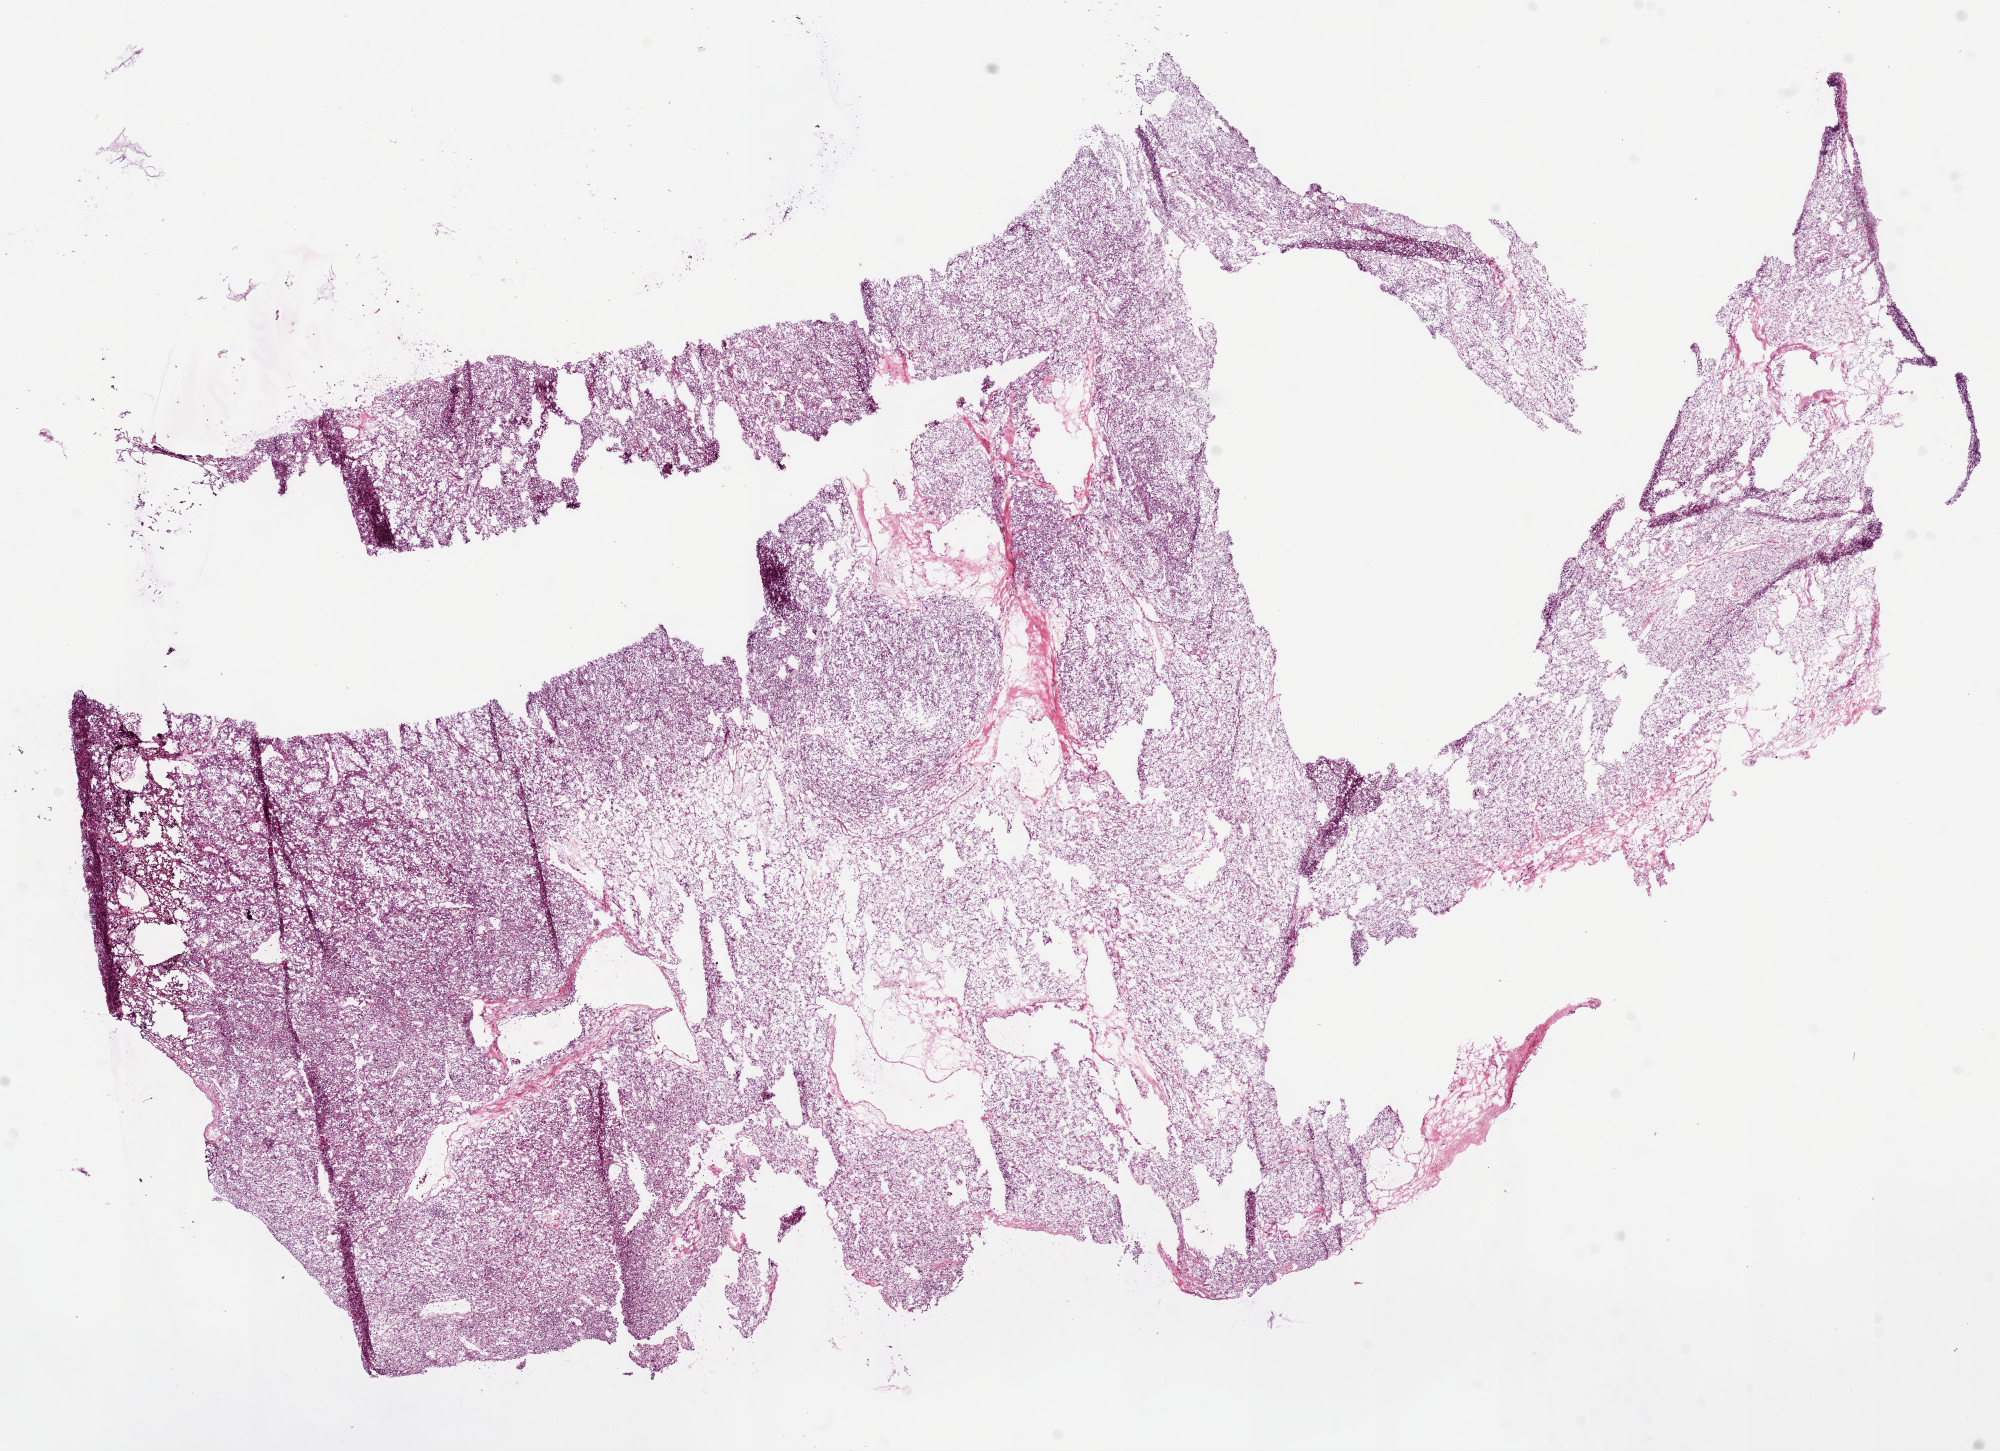
Digitized Hematoxylin and eosin (H&E) stained tissue section (whole slide), low-resolution overview of the scanned area, about 16.0 x 11.6 mm, frozen section from the bottom of the tissue portion, sample: primary tumour, kidney. Female, age 78 years at initial diagnosis. Histologic grade: G2 (moderately differentiated). Slide review estimates, as recorded: tumour cells 85%, tumour nuclei 85%, normal cells 0%, stromal cells 15%, necrosis 0%.
AJCC pathologic stage: II. Pathologic diagnosis: Clear cell adenocarcinoma, NOS.